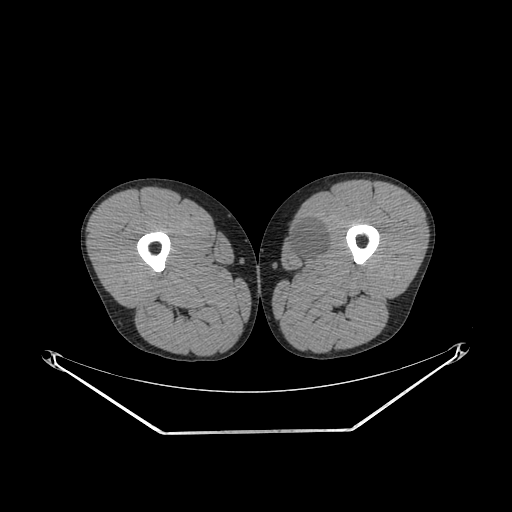
CT of an extremity soft-tissue mass (from a PET/CT study), one axial slice. Slice 256 of 311 in the series (ordered by position). Soft-tissue window (W 400 / L 40 HU). 3.75 mm slice thickness. 512 × 512 image matrix, field of view 500 × 500 mm. Male patient. Case-level facts recorded for this patient, not image findings: histological type: mixoid liposarcoma; grade: low; site of the primary tumour: left thigh.
Structures marked on this image (expert contour drawn on MRI and transferred to this co-registered scan by the dataset authors):
- gross tumour volume (mass): bounding box (x1, y1, x2, y2) in pixels: (288, 221, 328, 261)